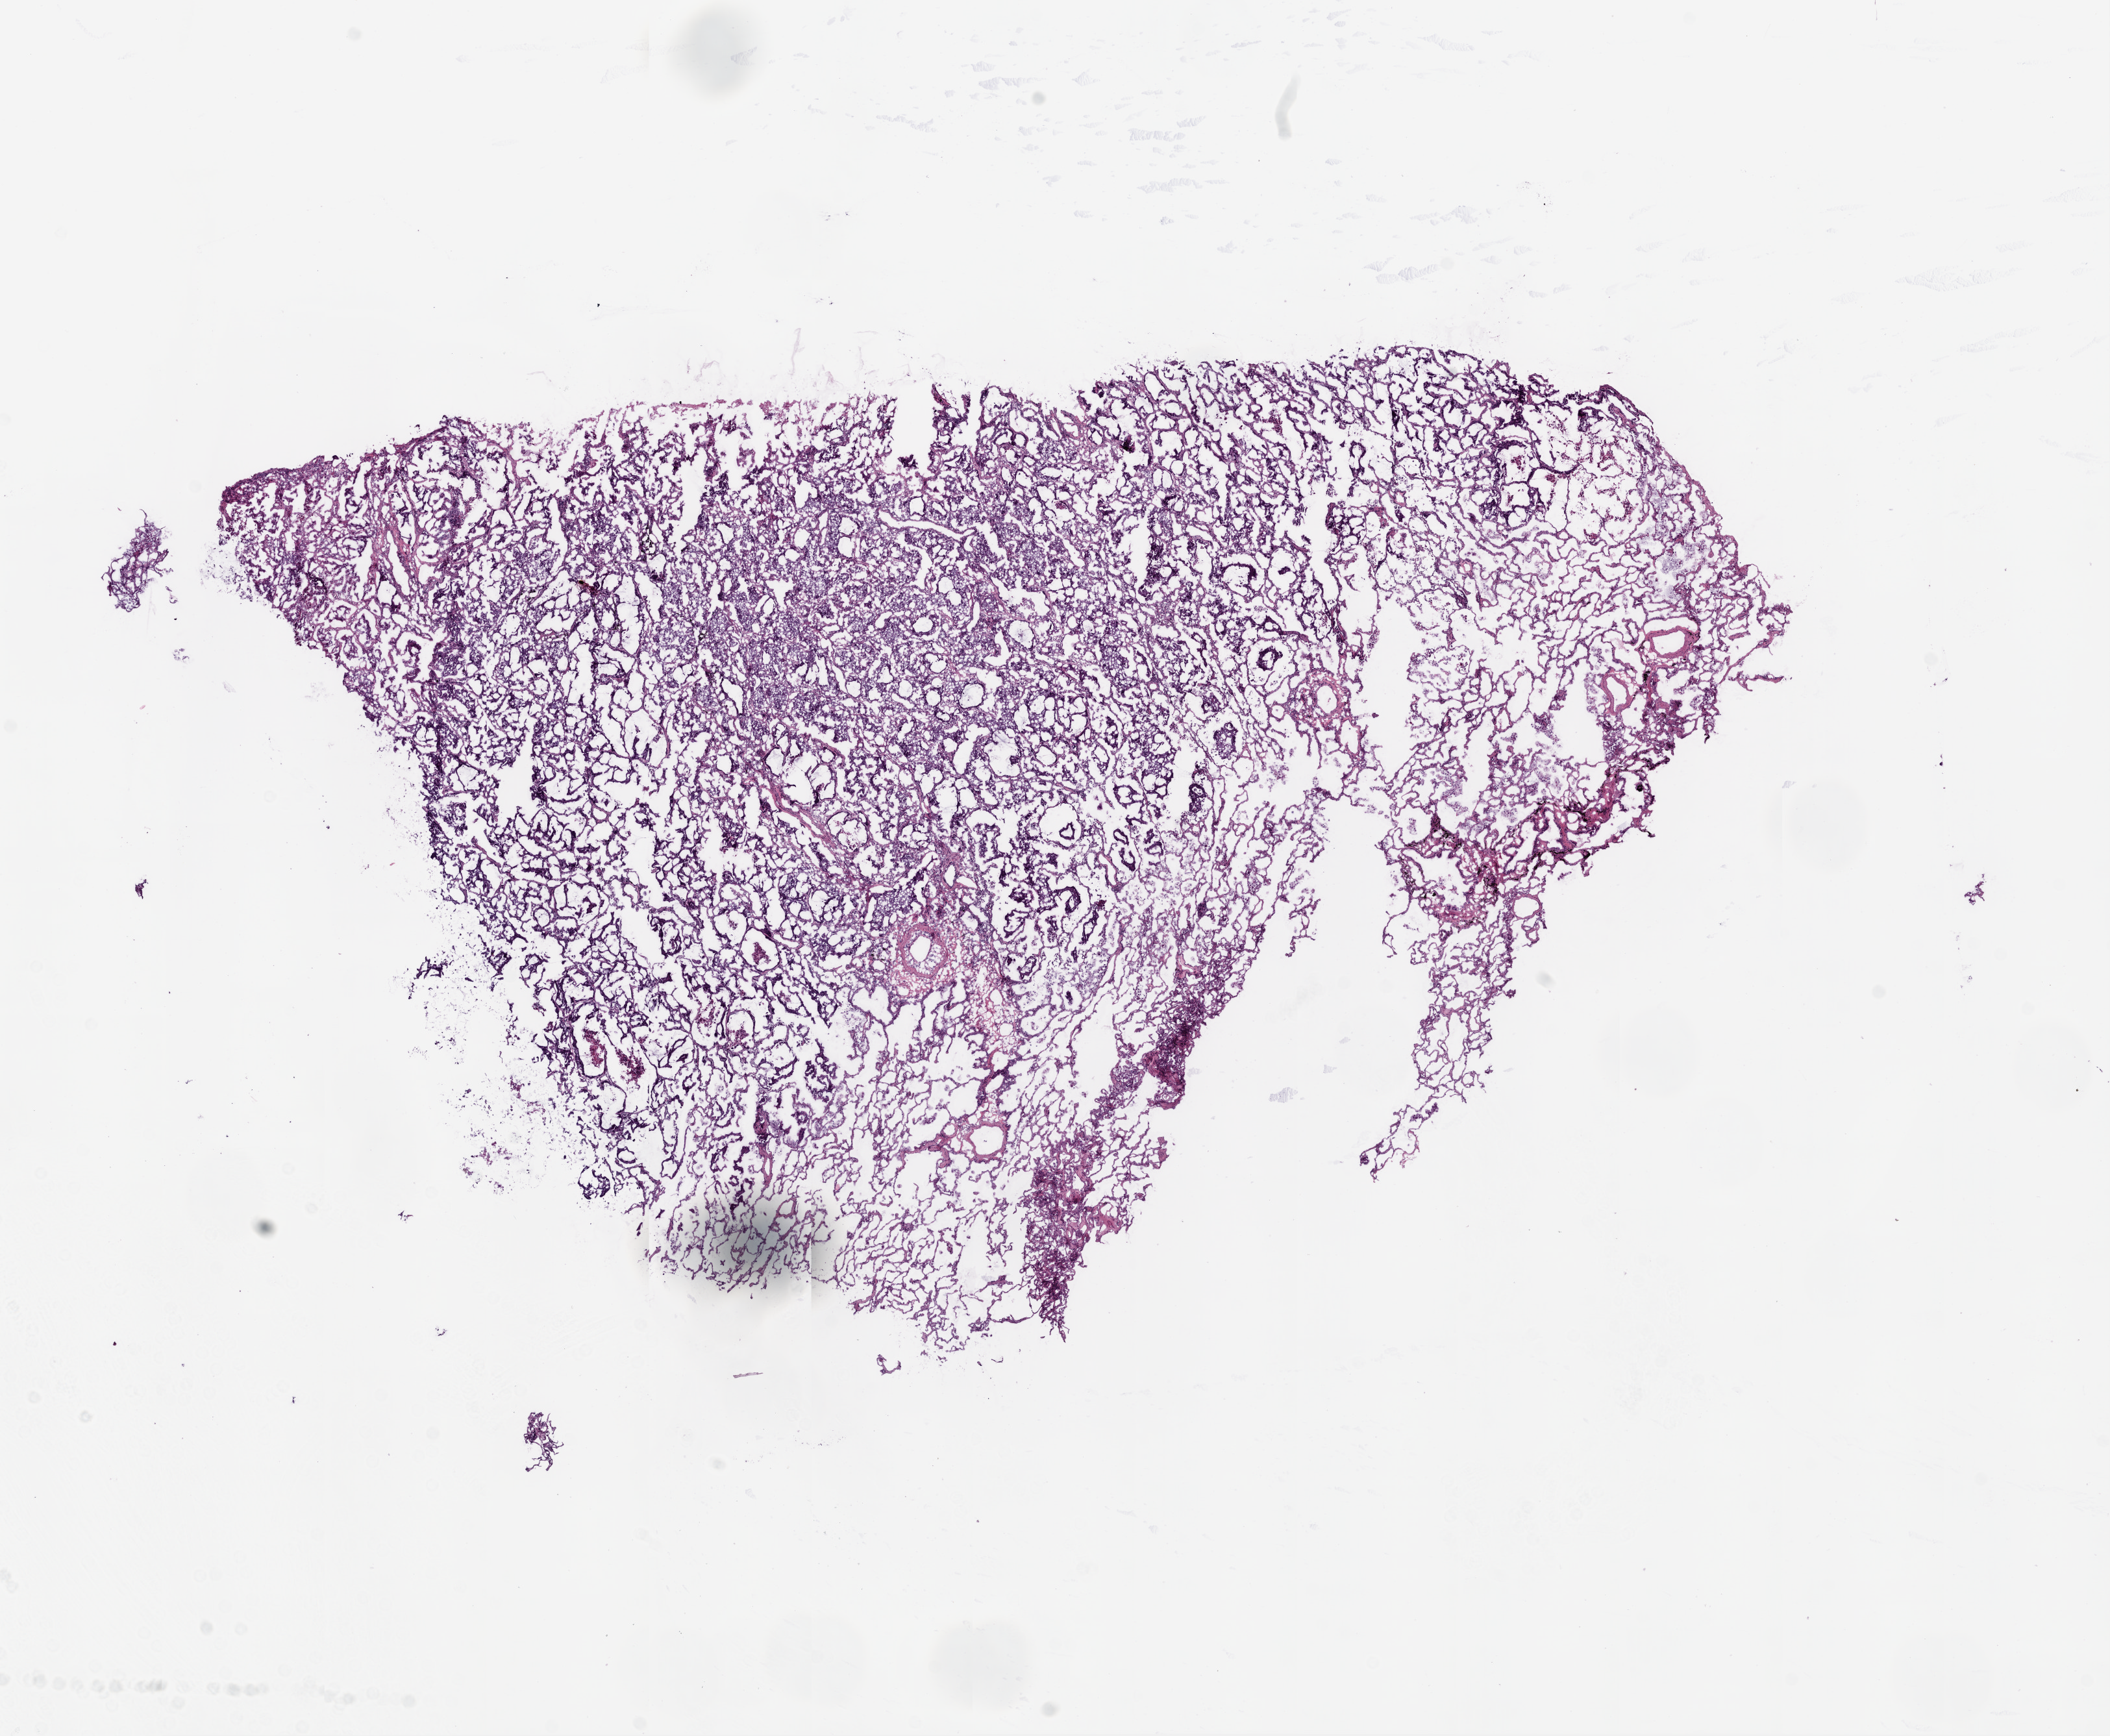
Whole-slide histology image, H&E, shown as a low-resolution overview of the whole scanned area (about 13.0 x 10.7 mm). Frozen section from the bottom of the tissue portion. Sample: primary tumour, lung. Patient: male, age at initial diagnosis 77 years. Slide review estimates, as recorded: tumour cells 70%, tumour nuclei 70%, normal cells 20%, stromal cells 5%, necrosis 5%.
Pathologic diagnosis: Adenocarcinoma, NOS (upper lobe, lung). TNM: T3 N2 M0. AJCC pathologic stage: IIIA (4th edition).